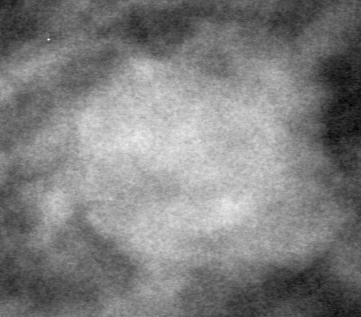
Cropped region of a digitized screen-film mammogram centred on a radiologist-marked abnormality; right breast; MLO view.
- Finding: mass, shape lobulated, margins circumscribed; BI-RADS assessment category 0 (incomplete: needs additional imaging); subtlety rating 4 on a 1 (subtle) to 5 (obvious) scale; pathology result (as recorded, not read from the image): malignant.